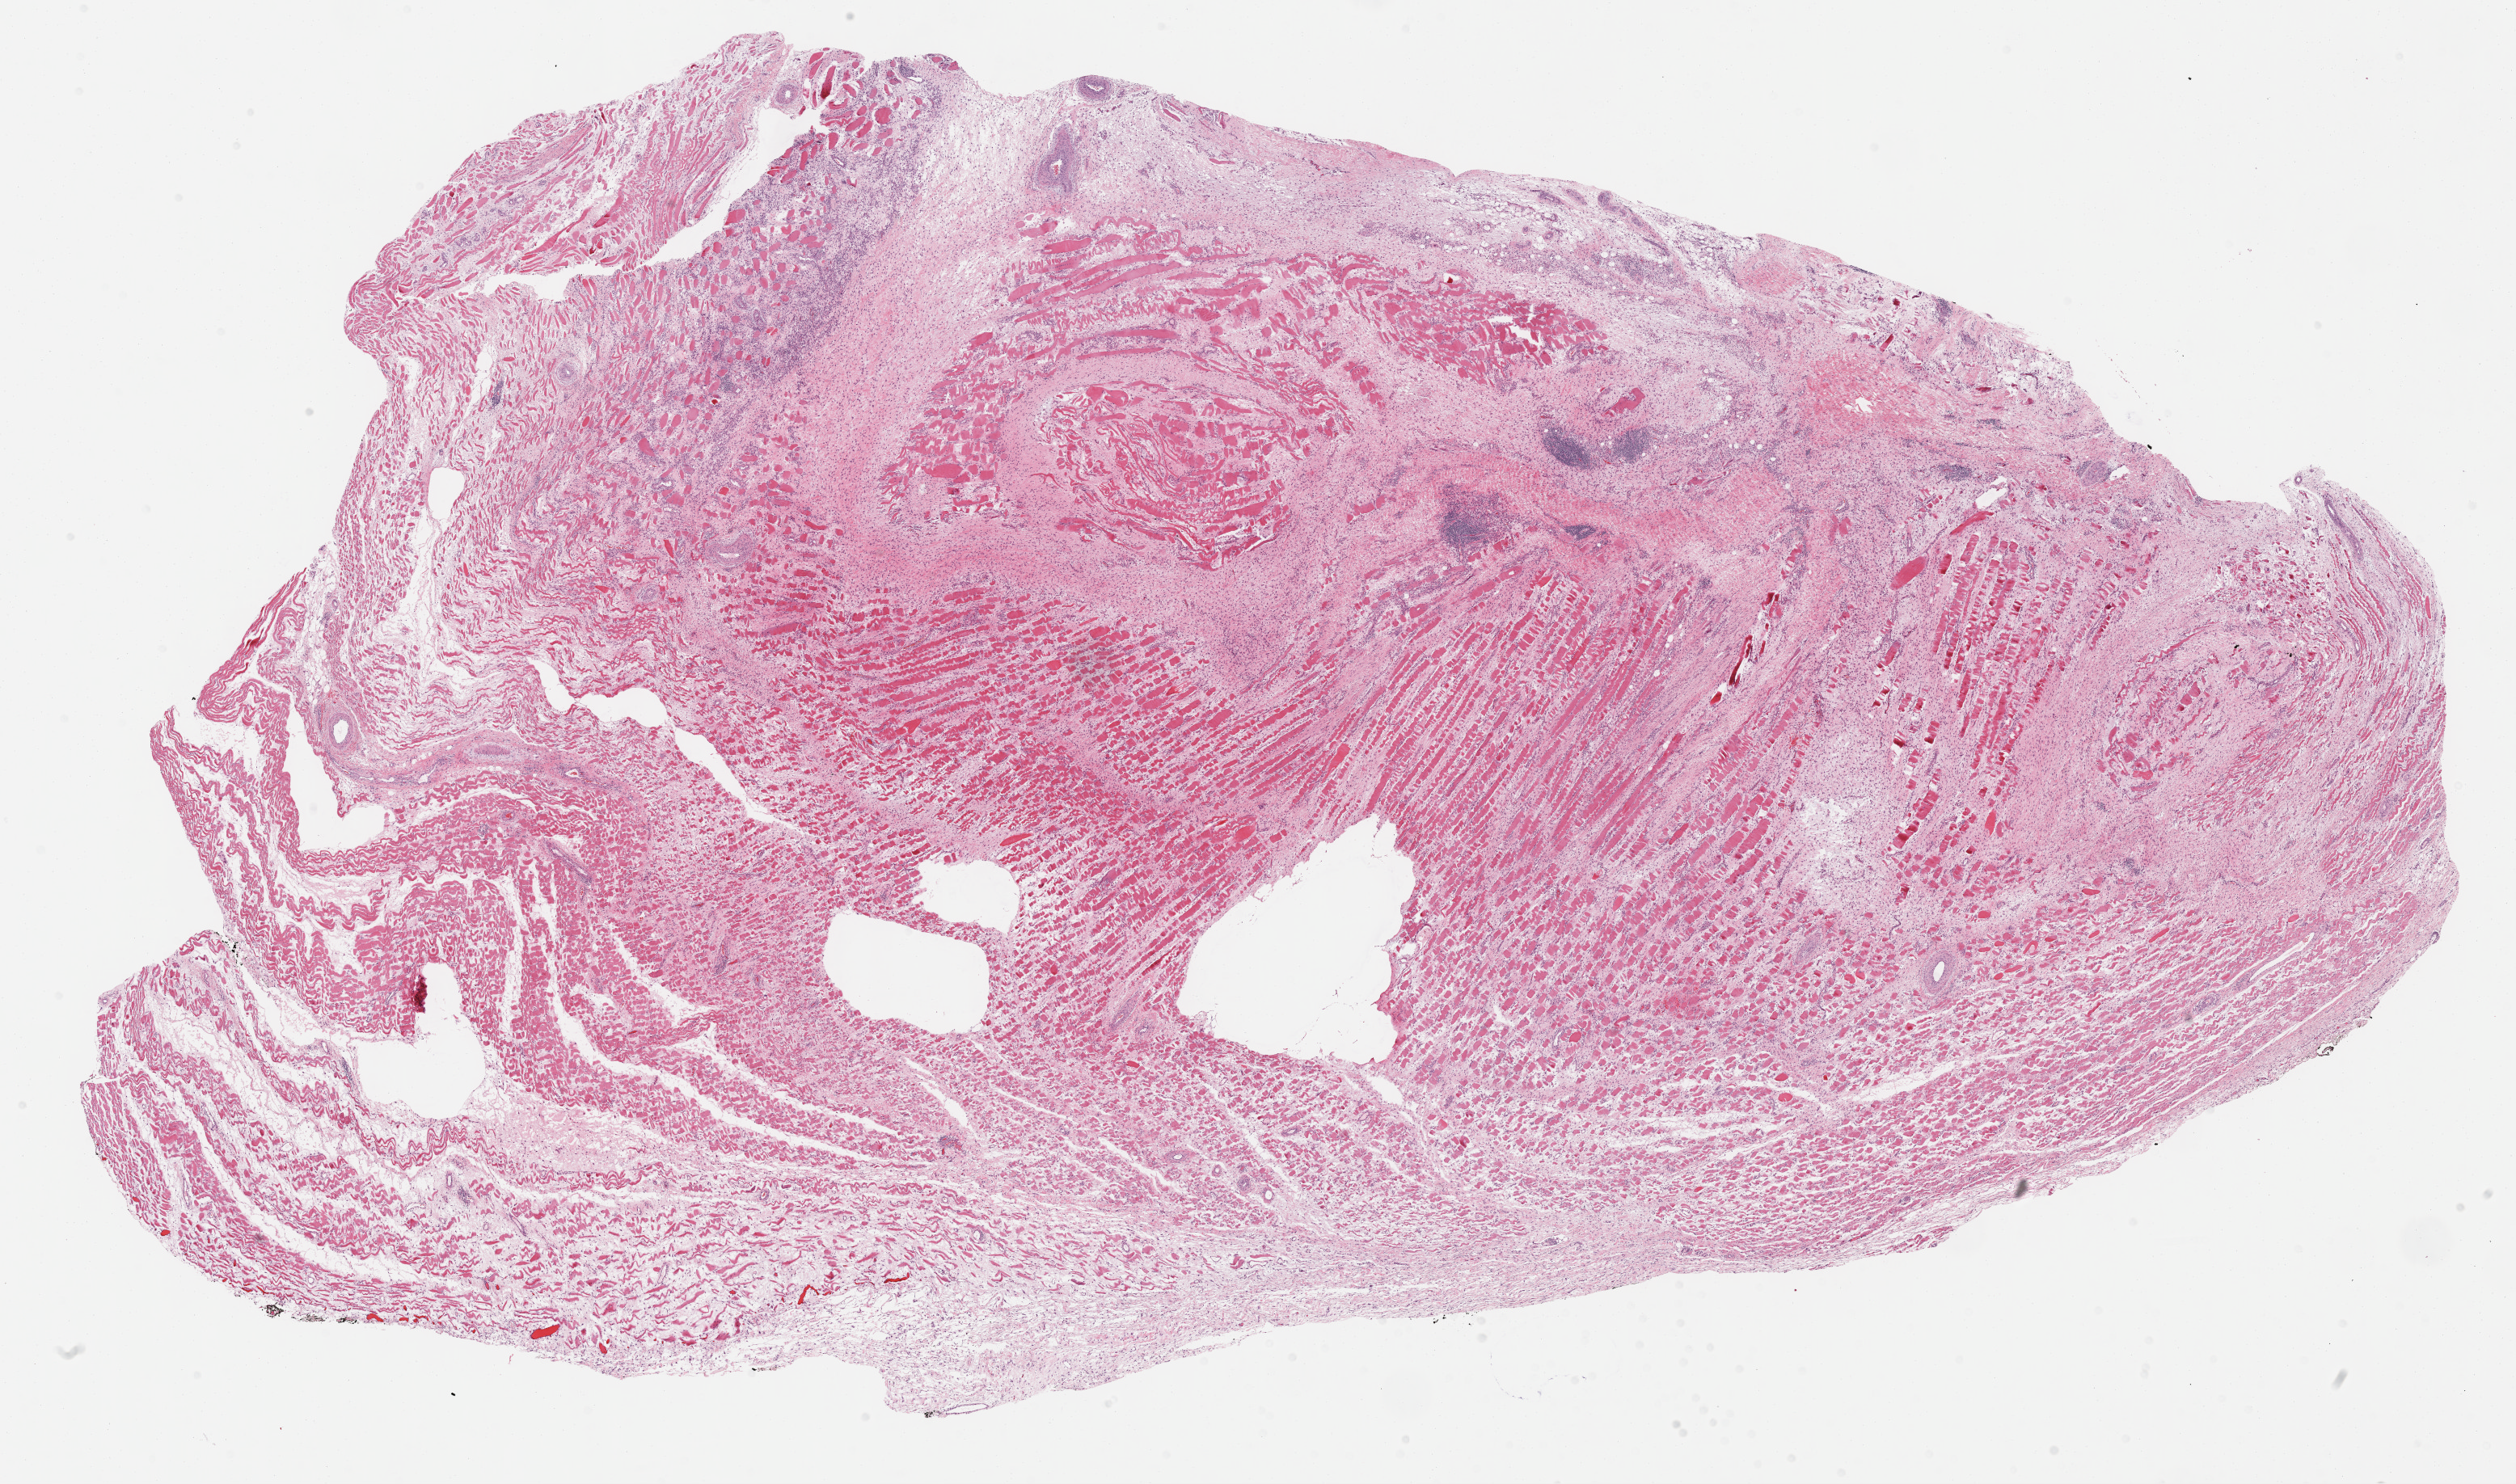
Digitized H&E-stained tissue section (whole slide), low-resolution overview of the scanned area, about 25.2 x 14.8 mm, formalin-fixed paraffin-embedded (FFPE) diagnostic section, sample: primary tumour, retroperitoneum and peritoneum. Patient: male, age at initial diagnosis 57 years.
Histologic diagnosis: Fibromyxosarcoma (retroperitoneum).